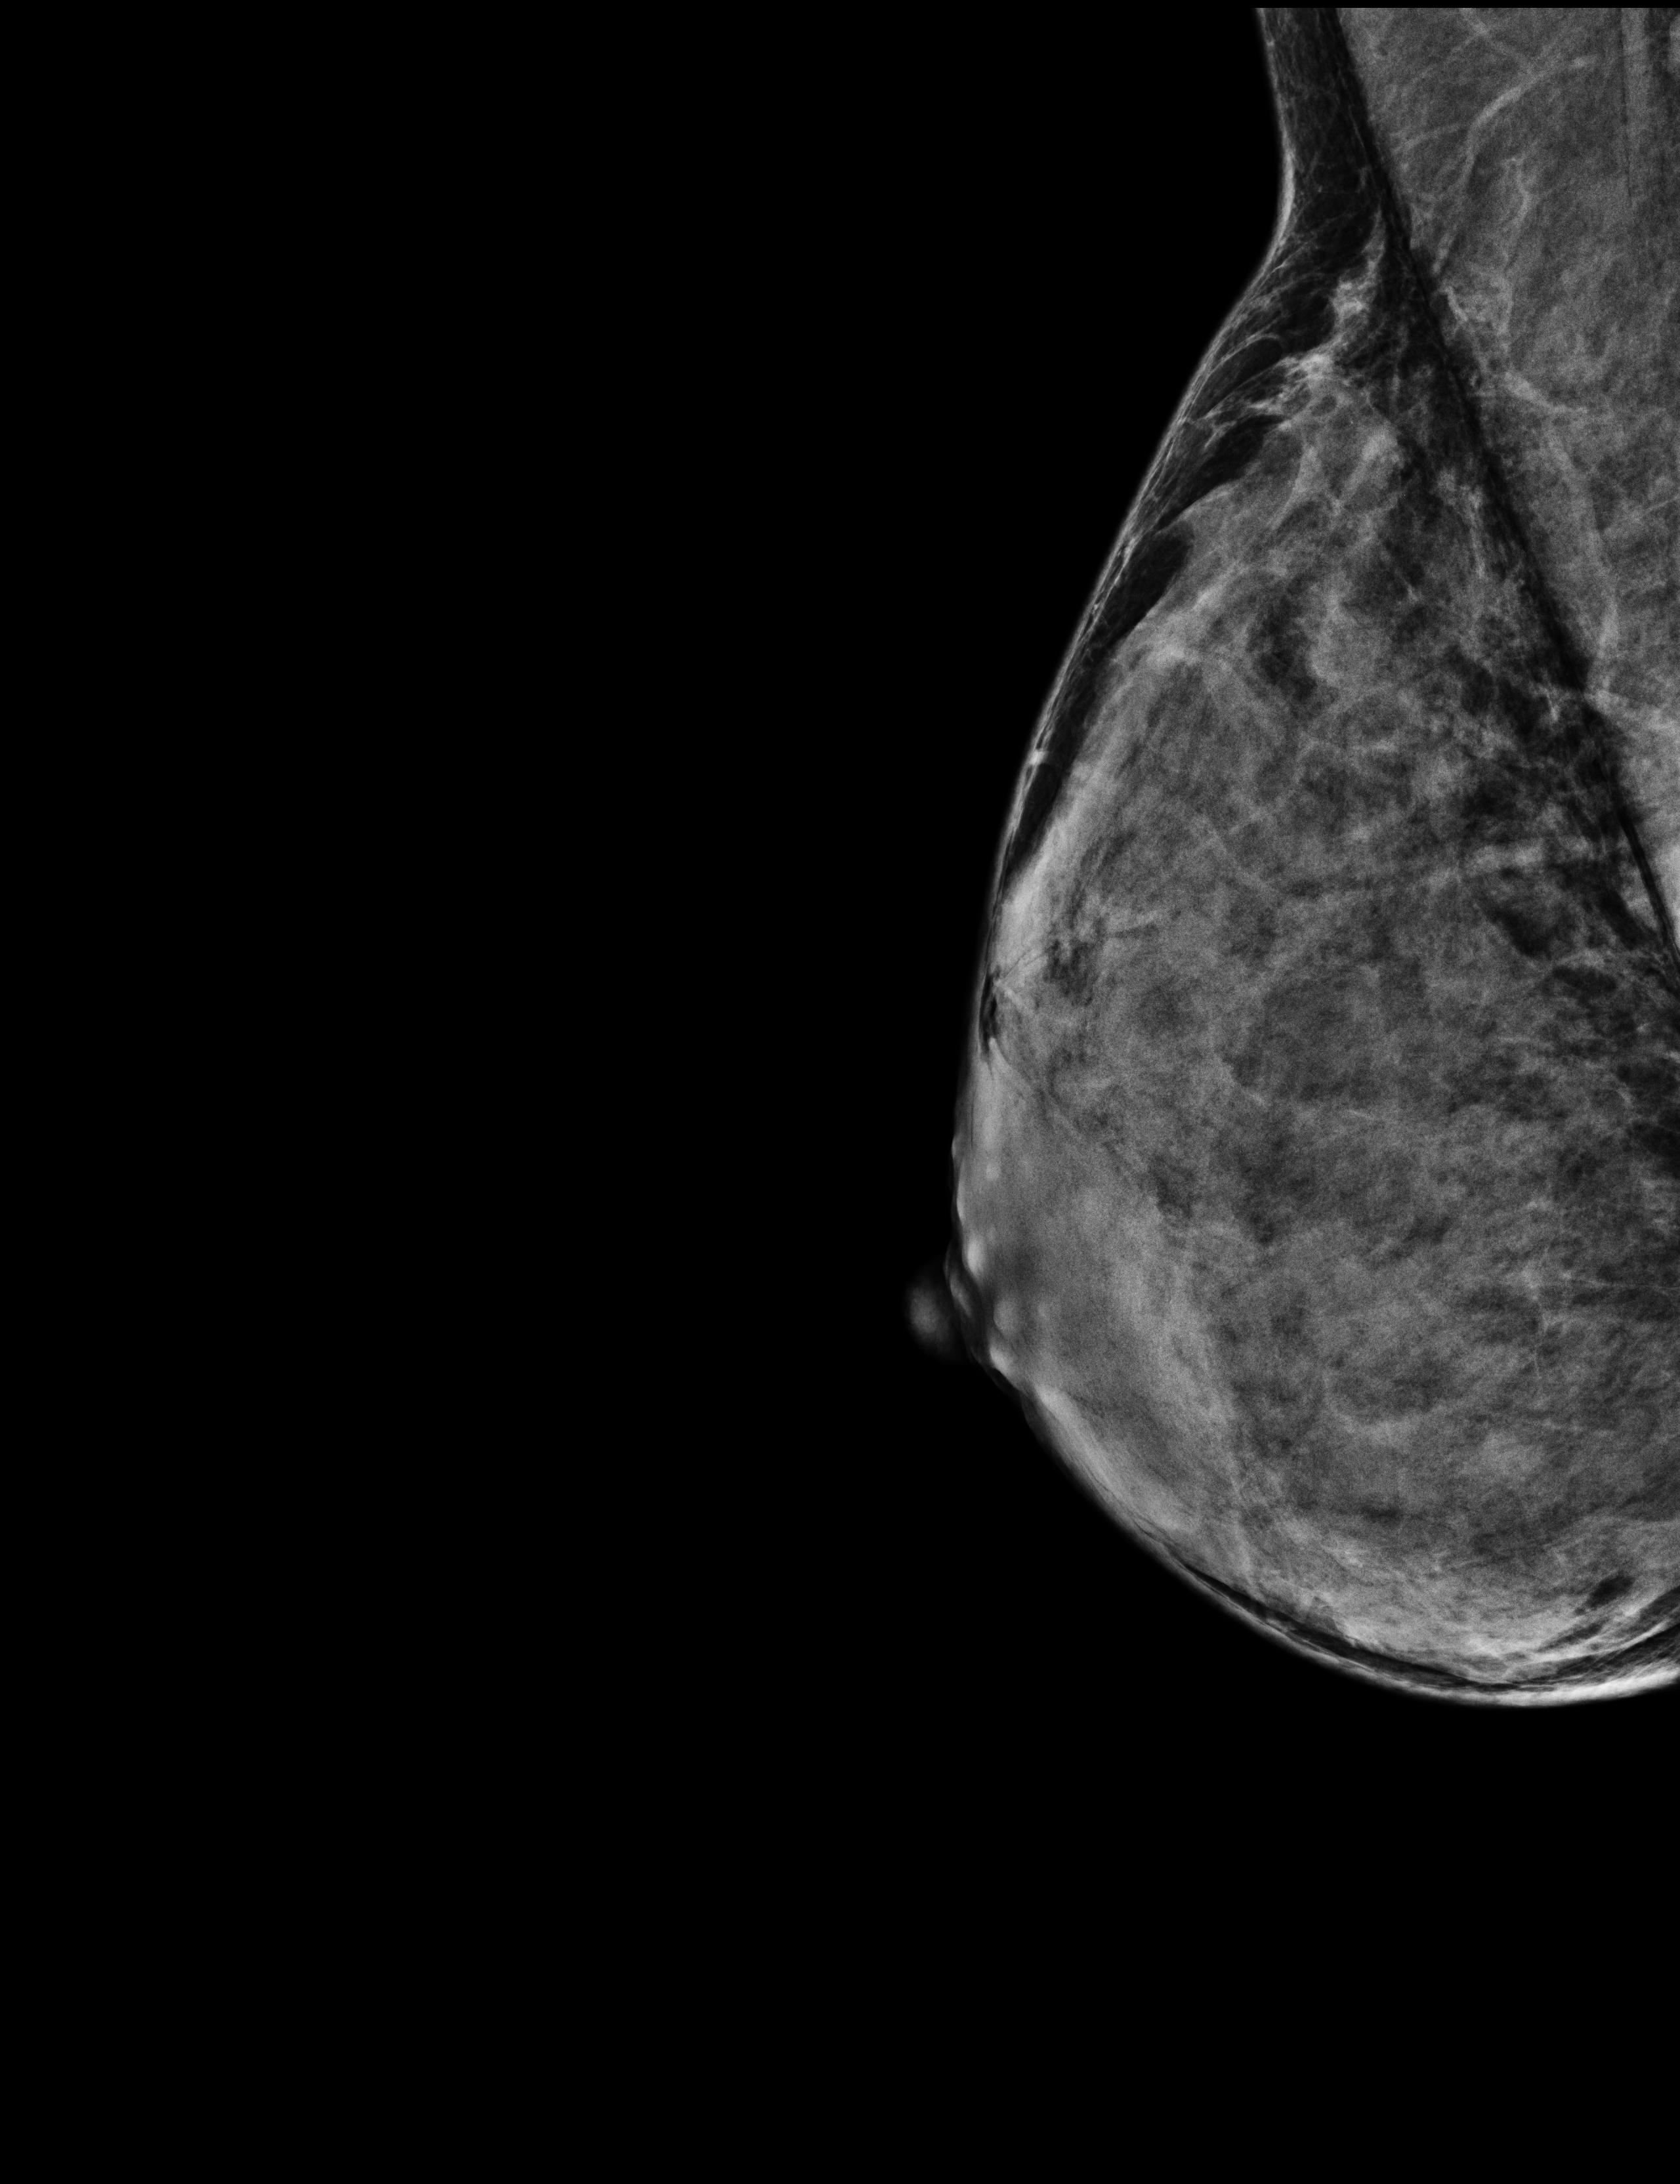
Annual screening mammography examination, compressed breast thickness 35 mm, system: Selenia Dimensions.
Image type: full-field digital mammogram. Breast: right. Projection: mediolateral oblique (MLO) view.